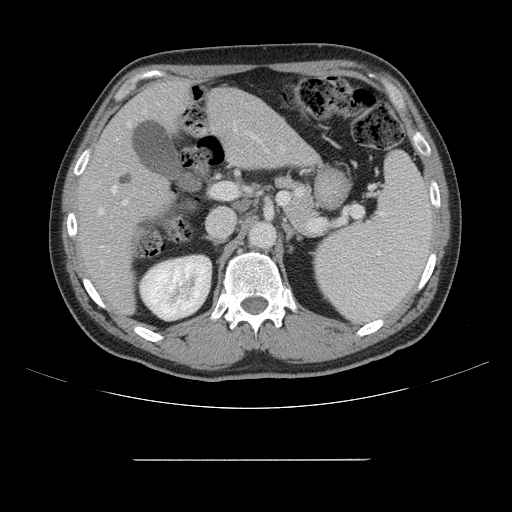
Contrast-enhanced abdominal CT, one axial slice; slice 89 of 164 in the series (ordered by position); 120 kVp; intravenous contrast given; soft-tissue window (W 400 / L 40 HU); 2.5 mm slice thickness; 512 × 512 image matrix, field of view 404 × 404 mm. Male patient, age 54 years. Case-level facts recorded for this patient, not image findings: diagnosis: colorectal cancer liver metastases, imaged before liver resection; multiple liver metastases: yes; largest metastasis: 1 cm; disease in both lobes: no.
Structures marked on this image (expert manual segmentation):
- hepatic veins: bounding box [x1, y1, x2, y2] px = [99, 146, 282, 263]
- liver: [80, 81, 315, 312]
- planned liver remnant (the part of the liver to remain after resection): [81, 81, 230, 312]
- portal vein (with intrahepatic branches): [117, 121, 261, 205]